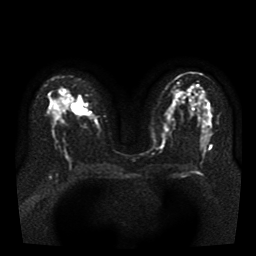
Breast MRI, one axial slice; position 23 of 41 along the scan axis; diffusion-weighted series; image 2 of 4 stored at this slice position (different b-values; order by instance number); 1.5 T; 256 × 256 image matrix, field of view 330 × 330 mm. Female patient.
Outlined on this slice (outlined manually by an expert reader):
- tumour on diffusion-weighted imaging: bounding box [x1, y1, x2, y2] px = [70, 102, 88, 114]